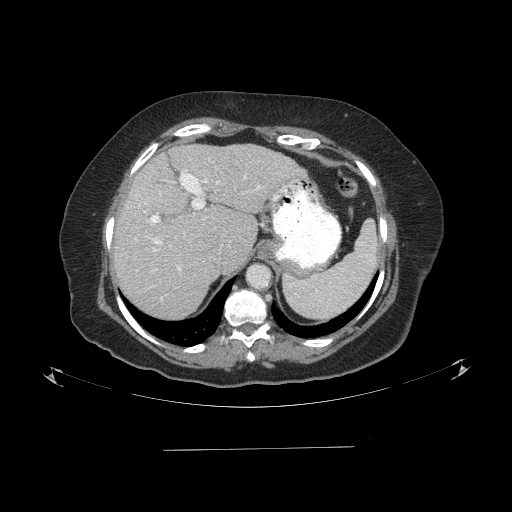
Contrast-enhanced abdominal CT (liver protocol), one axial slice; position 65 of 103 along the scan axis; reconstruction kernel STANDARD; one of 2 acquisitions stored at this slice position; soft-tissue window (W 400 / L 40 HU); 2.5 mm slice thickness; 512 × 512 image matrix, field of view 500 × 500 mm. From the clinical record (not read from this slice): diagnosis: hepatocellular carcinoma (patient treated with transarterial chemoembolisation; whether this scan precedes or follows treatment is not stated here); TNM stage (as recorded): Stage-IIIA.
Annotated regions visible in this slice (semi-automatically segmented with operator editing):
- abdominal aorta: bounding box (x1, y1, x2, y2) in pixels: (248, 264, 271, 288)
- liver parenchyma outside the tumour (the mass and vessels are separate outlines, so this box may not span the whole liver): (112, 144, 304, 318)
- liver vessels: (134, 169, 261, 300)